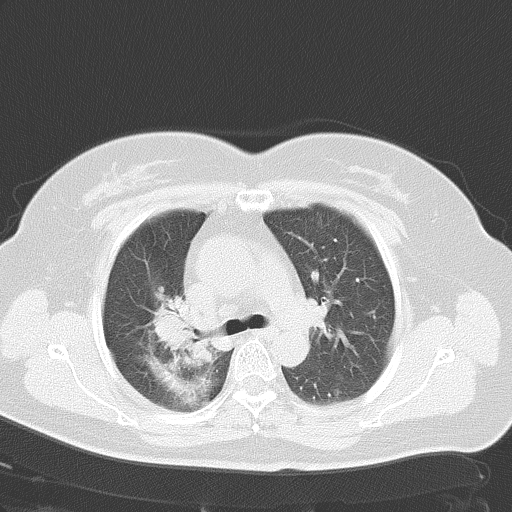
Chest CT, one axial slice; position 34 of 48 along the scan axis; reconstruction kernel B70f; 120 kVp; lung window (W 1500 / L -600 HU); 512 × 512 image matrix, field of view 353 × 353 mm. Female patient, age 50 years. From the clinical record (not read from this slice): clinical TNM (as recorded): T2a N0 M1a.
Annotated regions visible in this slice (rectangle marked by the reading radiologist):
- lung tumour (recorded histology: adenocarcinoma): bounding box (x1, y1, x2, y2) in pixels: (145, 289, 216, 372)